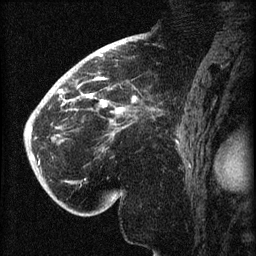
Breast MRI (dynamic contrast-enhanced), one sagittal slice; dynamic contrast-enhanced series, image 2 of 3 at this slice position (ordered by acquisition); 1.5 T; TE 4.2 ms, TR 8.2 ms; 256 × 256 image matrix, field of view 180 × 180 mm. Patient: female, 71 years.
Annotated regions visible in this slice (semi-automatically segmented with operator editing):
- analysis volume of interest (the breast-tissue region the enhancement analysis was run in; not a lesion): bounding box [x1, y1, x2, y2] px = [40, 72, 148, 196]
- tumour enhancement mask (voxels above the 70 % enhancement threshold inside the analysis volume of interest): [58, 78, 137, 114]